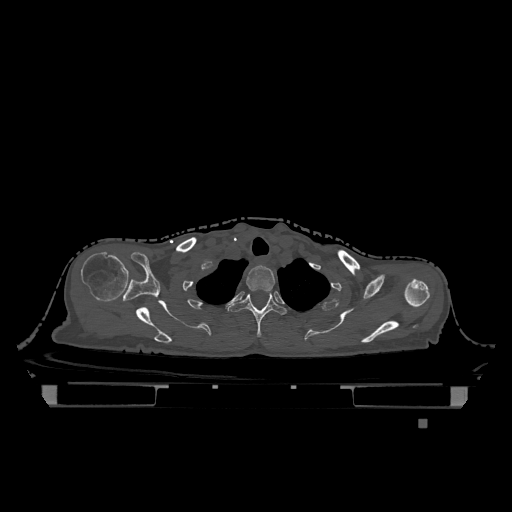
CT including the spine, one axial slice. Slice 974 of 1317 in the series (ordered by position). Bone window (W 1800 / L 400 HU). 0.5 mm slice thickness. 512 × 512 image matrix, field of view 500 × 500 mm. Female patient, age 74 years. From the clinical record (not read from this slice): primary cancer: lung; vertebrae with lytic lesions (as recorded): T1, T4, T5, T6, L4, L5.
Structures marked on this image (semi-automatically segmented with operator editing):
- T1 vertebra: bounding box (x1, y1, x2, y2) in pixels: (246, 265, 275, 293)
- T2 vertebra: (228, 291, 287, 337)